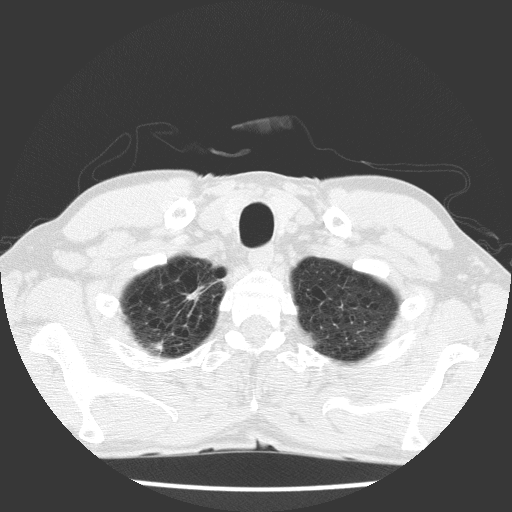
Low-dose screening chest CT, axial slice; first (baseline) screen; lung window (W 1500 / L -600 HU); 2 mm slice thickness; lung (sharp) reconstruction kernel (FC51); 512 × 512 image matrix, field of view 325 × 325 mm. Male participant, aged 63 years at enrolment. Current smoker at enrolment.
Lesion marked by an expert reader, bounding box [x1, y1, x2, y2] px = [150, 272, 221, 343]. Screening reader's record for this exam: no non-calcified nodule ≥4 mm recorded. Participant outcome: lung cancer diagnosed 741 days after this screen — adenocarcinoma, NOS, right upper lobe, moderately differentiated (G2), stage IIIB (AJCC 6th edition), 17 mm at pathology.